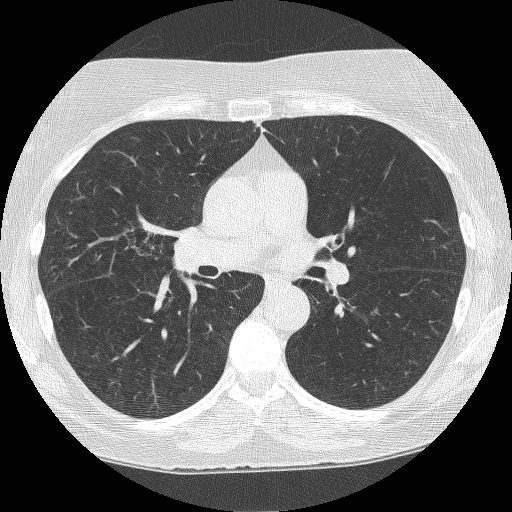
Chest CT (low-dose screening protocol), one axial image; second annual screen; lung window (W 1500 / L -600 HU). Female, age 64 years at enrolment.
Expert-annotated lung lesion, bounding box <117,206,200,286> (left, top, right, bottom; pixels). The screening reader recorded 4 non-calcified nodules or masses ≥4 mm on this exam (right upper lobe, right upper lobe, right upper lobe, left upper lobe); which of them this box marks is not recorded. Participant outcome: lung cancer diagnosed 381 days after this screen (after the third annual screen) — adenocarcinoma, NOS, right upper lobe, right middle lobe, right hilum, stage IV (AJCC 6th edition), 85 mm at pathology.